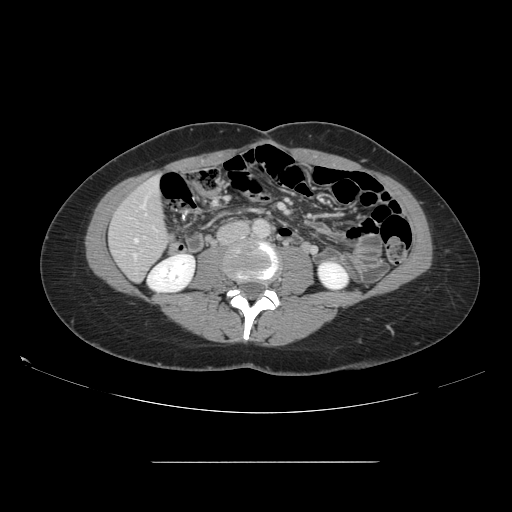
Contrast-enhanced abdominal CT, one axial slice; position 36 of 151 along the scan axis; 120 kVp; intravenous contrast given; soft-tissue window (W 400 / L 40 HU); 2.5 mm slice thickness; 512 × 512 image matrix, field of view 421 × 421 mm. Female patient, age 46 years. Case-level facts recorded for this patient, not image findings: diagnosis: colorectal cancer liver metastases, imaged before liver resection; multiple liver metastases: yes; largest metastasis: 3 cm; disease in both lobes: yes.
Annotated regions visible in this slice (outlined manually by an expert reader):
- hepatic veins: bounding box (x1, y1, x2, y2) in pixels: (135, 239, 137, 241)
- liver: (111, 178, 169, 280)
- planned liver remnant (the part of the liver to remain after resection): (111, 178, 169, 280)